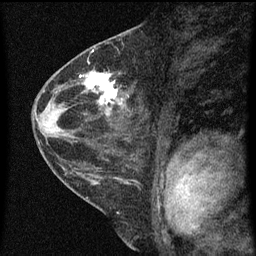
Breast MRI (dynamic contrast-enhanced), one sagittal slice. Position 30 of 60 along the scan axis. Dynamic contrast-enhanced series, image 2 of 3 at this slice position (ordered by acquisition). 1.5 T. TE 4.2 ms, TR 8 ms. 256 × 256 image matrix. Patient: female, 48 years.
Outlined on this slice (semi-automatic segmentation, software-assisted and operator-edited):
- analysis volume of interest (the breast-tissue region the enhancement analysis was run in; not a lesion): bounding box <82,70,126,125> (left, top, right, bottom; pixels)
- tumour enhancement mask (voxels above the 70 % enhancement threshold inside the analysis volume of interest): <82,74,123,105>